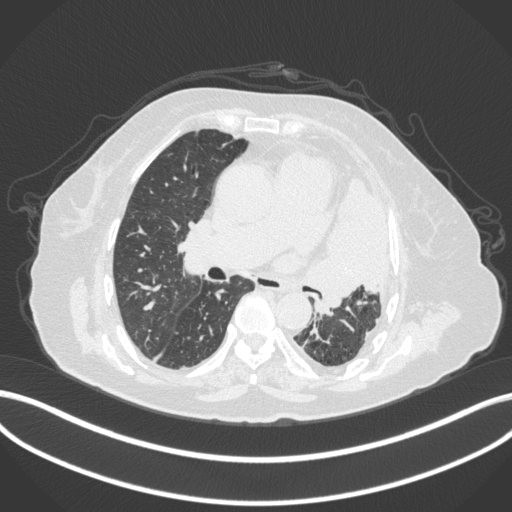
Chest CT, one axial slice. Reconstruction kernel B31f. 120 kVp. Lung window (W 1500 / L -600 HU). 1 mm slice thickness. 512 × 512 image matrix, field of view 400 × 400 mm. Female patient, age 75 years. Case-level facts recorded for this patient, not image findings: clinical TNM (as recorded): T3 N3 M1.
Annotated regions visible in this slice (rectangle marked by the reading radiologist):
- lung tumour (recorded histology: adenocarcinoma): bounding box (x1, y1, x2, y2) in pixels: (301, 174, 390, 317)